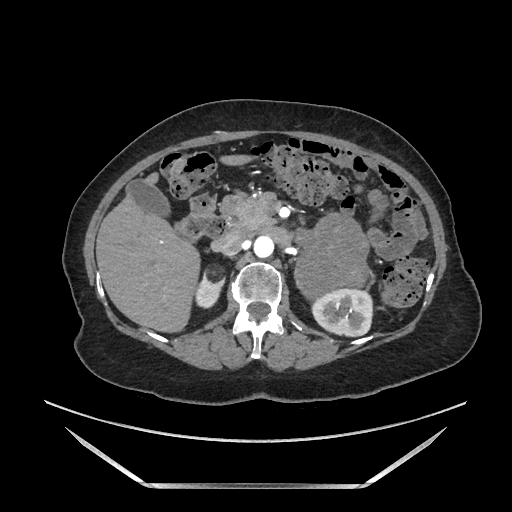
Contrast-enhanced abdominal CT, one axial slice; slice 95 of 205 in the series (ordered by position); soft-tissue window (W 400 / L 40 HU); 1.25 mm slice thickness; 512 × 512 image matrix, field of view 440 × 440 mm. Female patient. From the clinical record (not read from this slice): diagnosis: adrenocortical carcinoma; tumour side: left adrenal; tumour size at pathology: 12.5 cm; Ki-67 index: 39 %; stage (as recorded): 3.
Structures marked on this image (semi-automatic segmentation, software-assisted and operator-edited):
- mass: bounding box <299,217,366,297> (left, top, right, bottom; pixels)